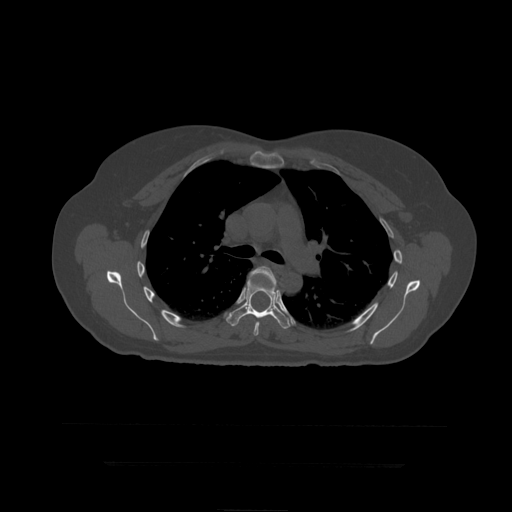
CT including the spine, one axial slice. Slice 308 of 399 in the series (ordered by position). 120 kVp. Bone window (W 1800 / L 400 HU). 1.25 mm slice thickness. 512 × 512 image matrix, field of view 450 × 450 mm. Patient age 41 years. From the clinical record (not read from this slice): primary cancer: breast.
Structures marked on this image (semi-automatic segmentation, software-assisted and operator-edited):
- T6 vertebra: bounding box (x1, y1, x2, y2) in pixels: (250, 266, 277, 336)
- T7 vertebra: (225, 273, 291, 330)